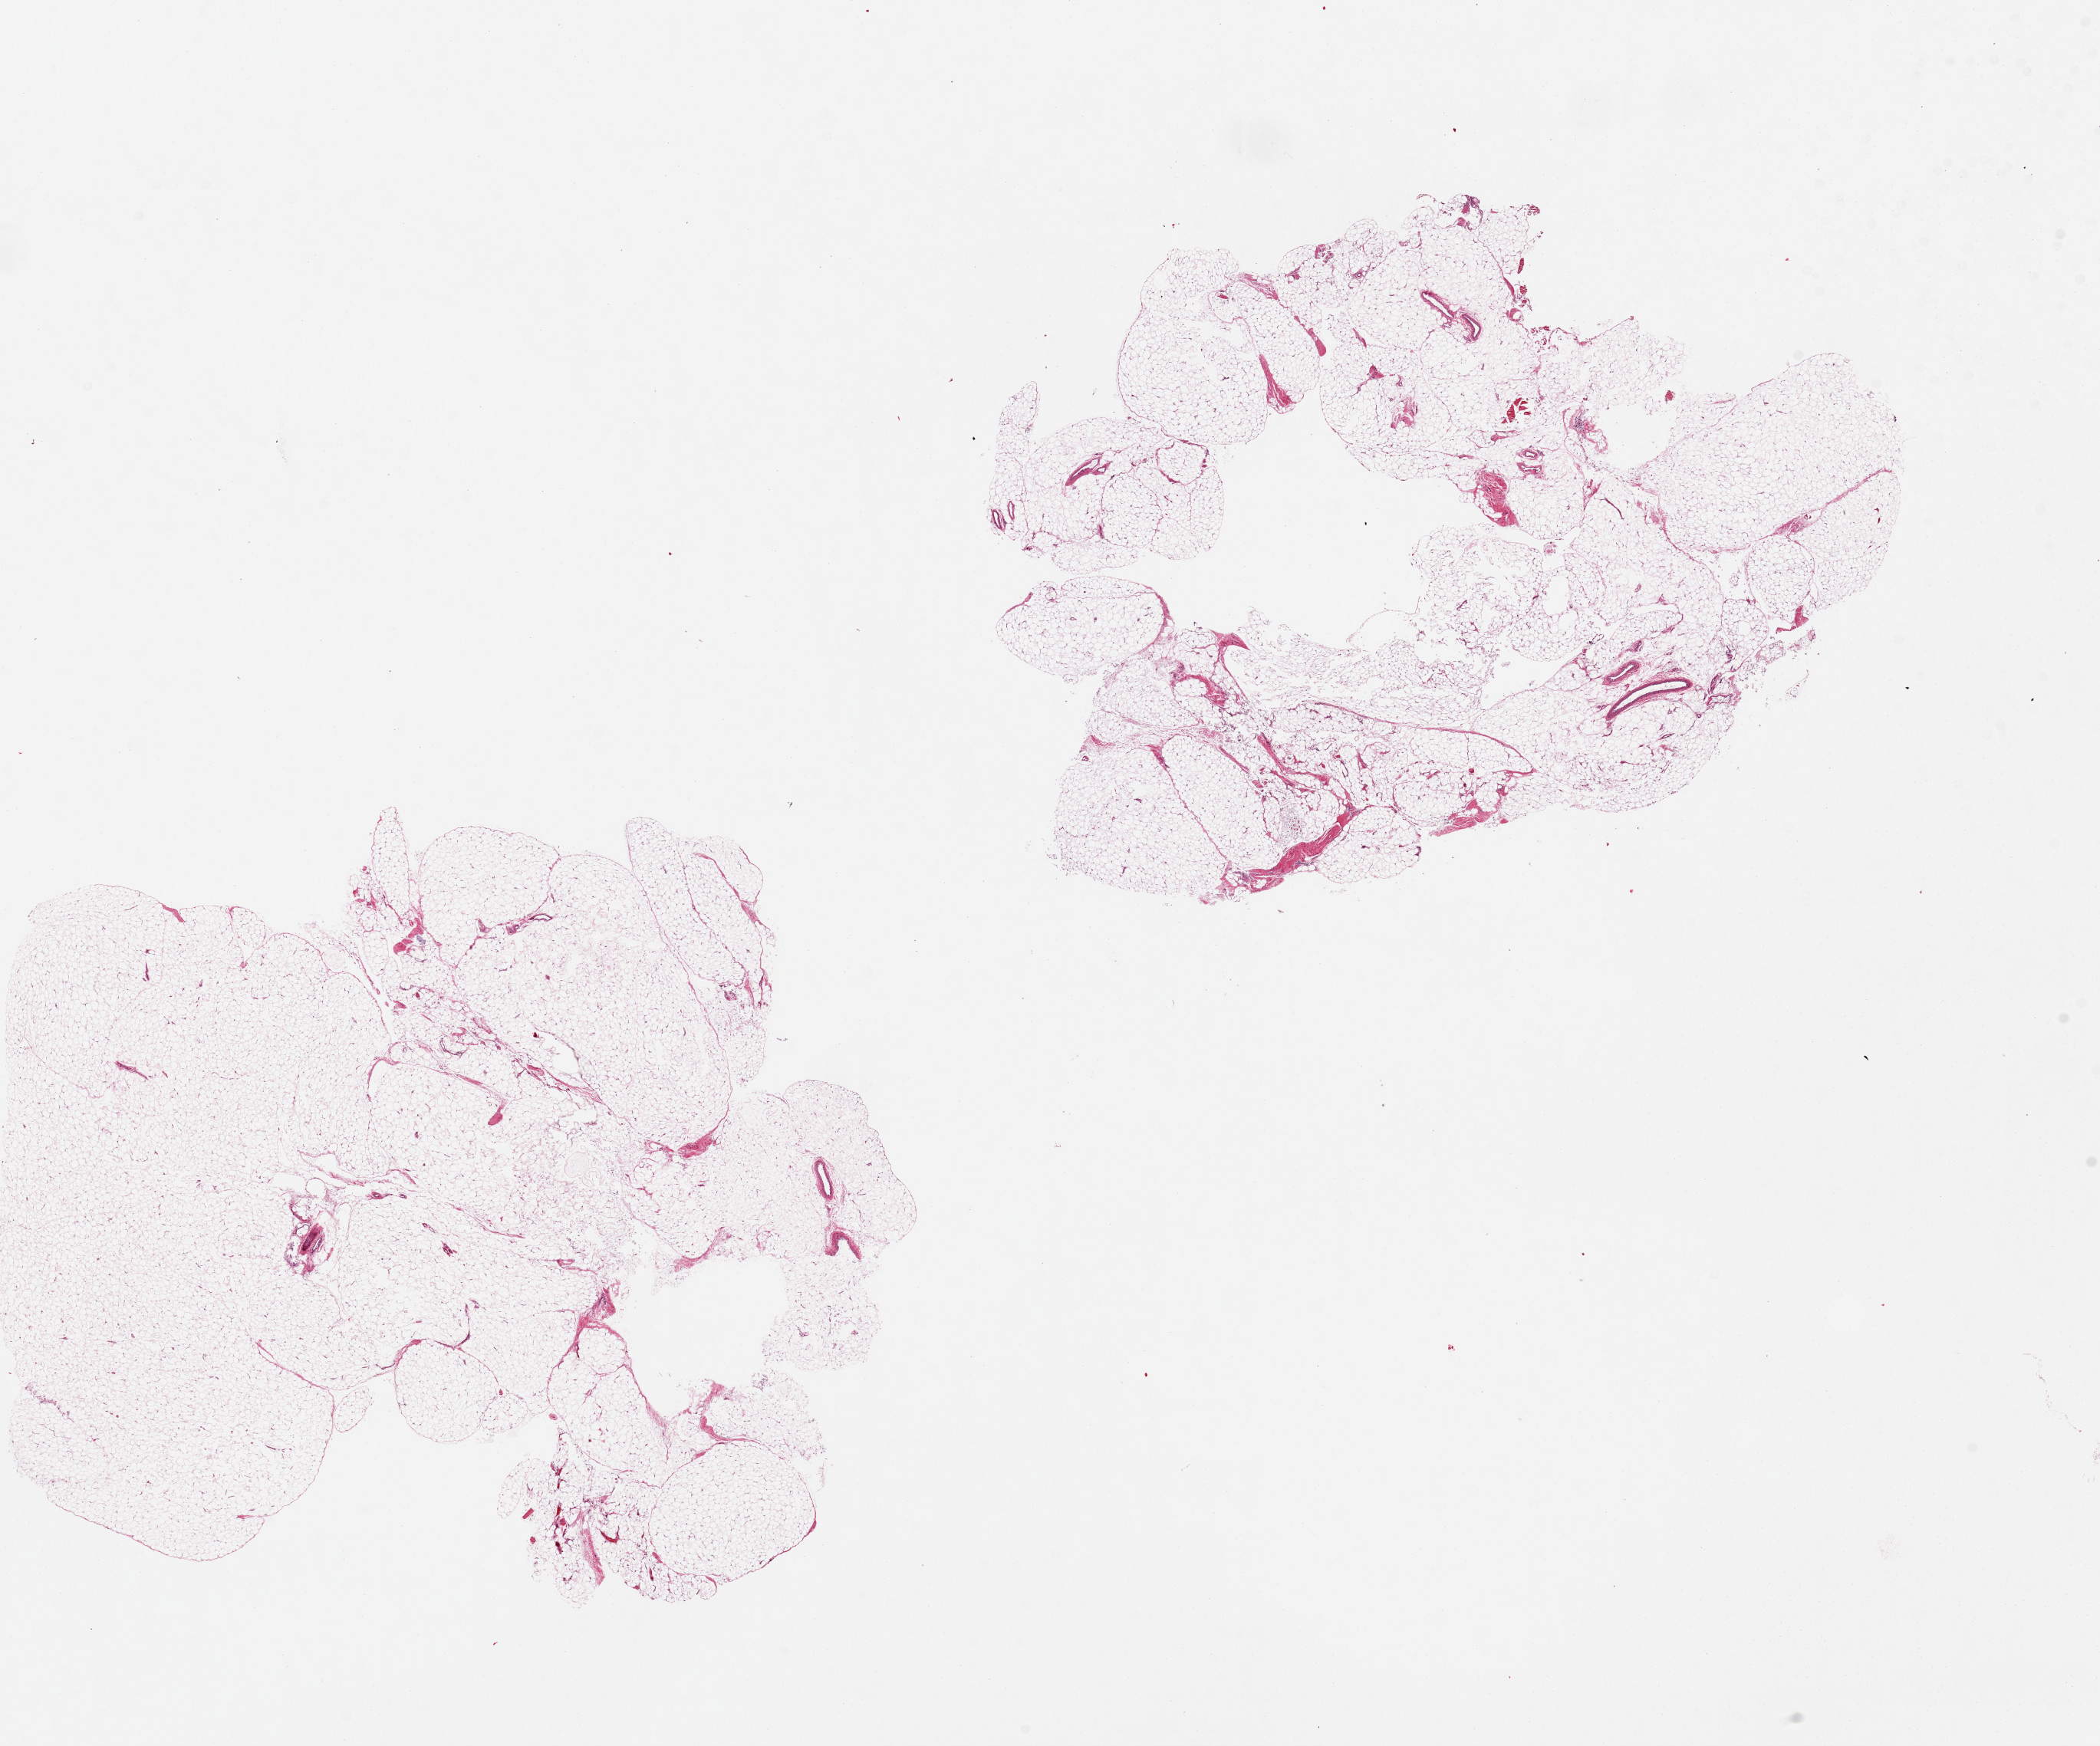
Hematoxylin and eosin (H&E) whole-slide image, brightfield — whole scanned area (about 21.7 x 18.0 mm, slide scanned at 20x) shown as a low-resolution overview, PAXgene-fixed, paraffin-embedded tissue, section of omentum (target tissue), donor tissue sample. Male donor.
Reviewer comment on this tissue sample: 2 pieces; 1 has central hole.